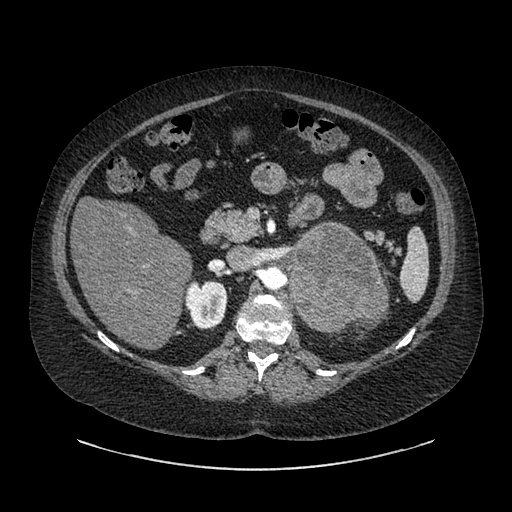
Contrast-enhanced abdominal CT, one axial slice; position 544 of 769 along the scan axis; intravenous contrast given; soft-tissue window (W 400 / L 40 HU); 0.62 mm slice thickness; 512 × 512 image matrix, field of view 460 × 460 mm. Patient: female, 61 years. Case-level facts recorded for this patient, not image findings: diagnosis: adrenocortical carcinoma; tumour side: left adrenal; tumour size at pathology: 13 cm; Ki-67 index: 79 %; stage (as recorded): 2.
Outlined on this slice (semi-automatically segmented with operator editing):
- mass: bounding box (x1, y1, x2, y2) in pixels: (291, 225, 383, 330)